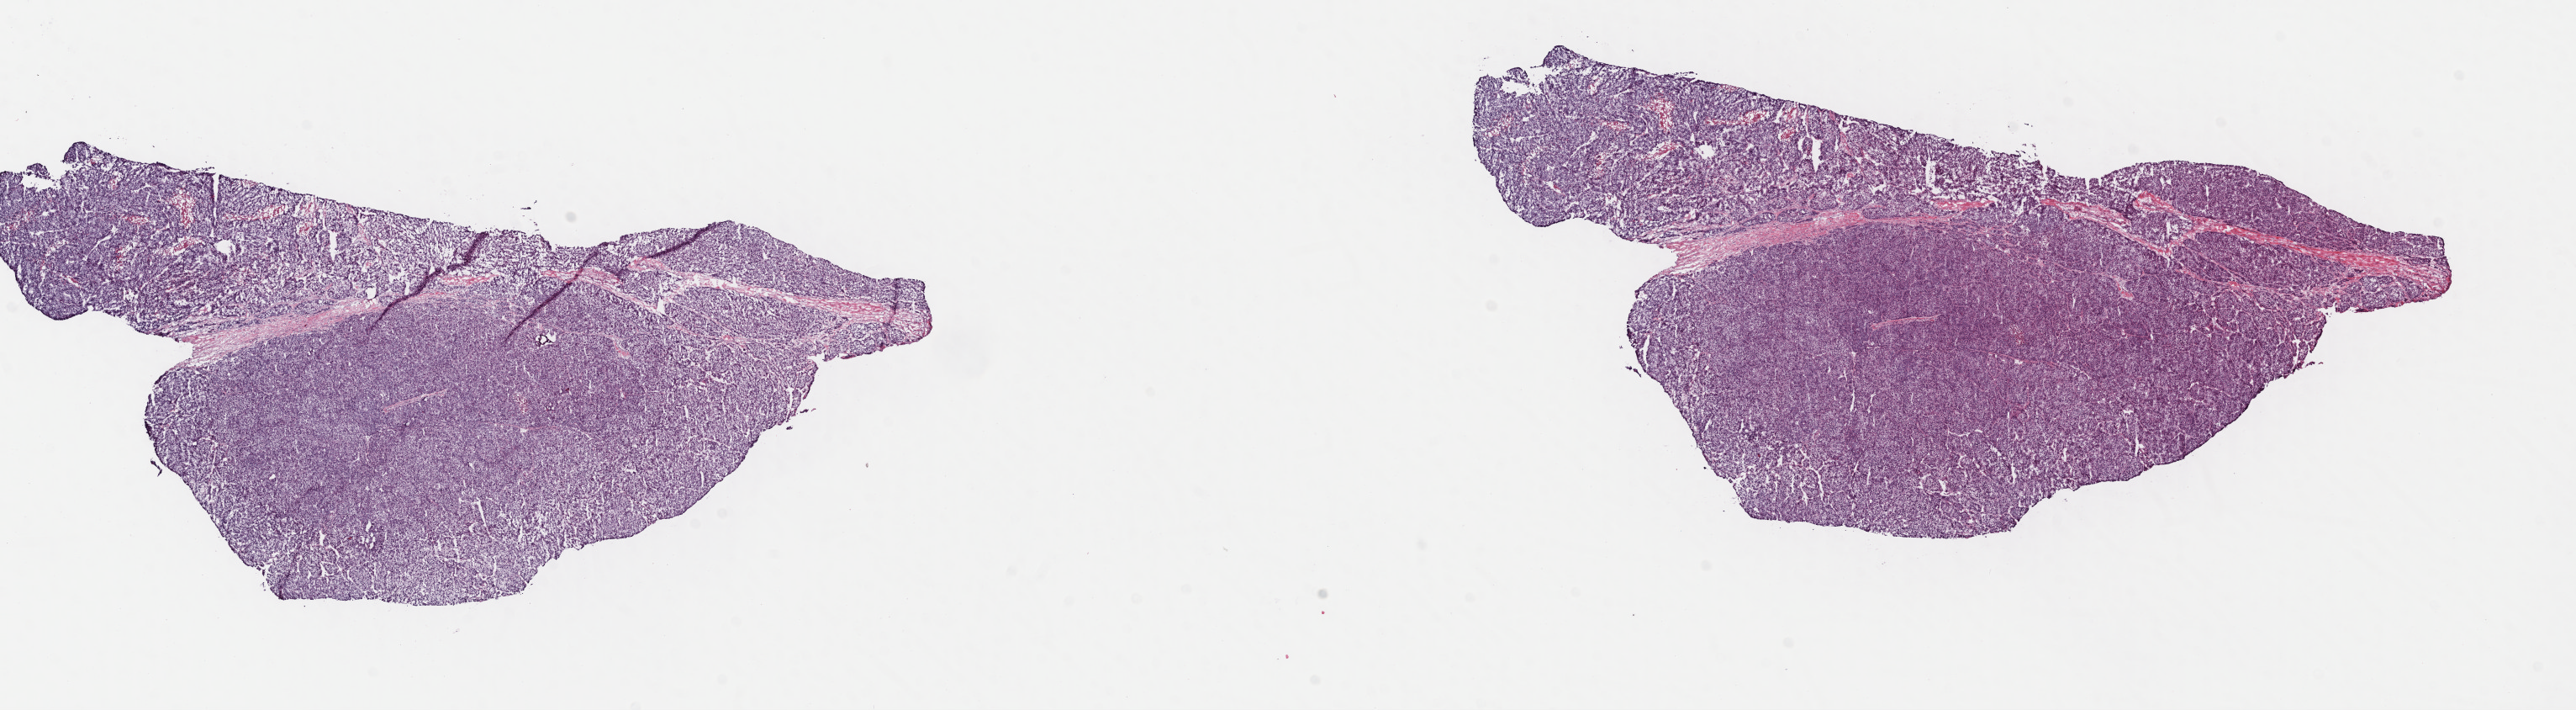
H&E whole-slide image — low-resolution overview of the scanned area, about 24.1 x 6.6 mm (from a 40x scan); frozen section; primary tumour sample from the liver. Patient: female, age at initial diagnosis 26 years.
Pathologic diagnosis: Hepatocellular carcinoma, NOS.